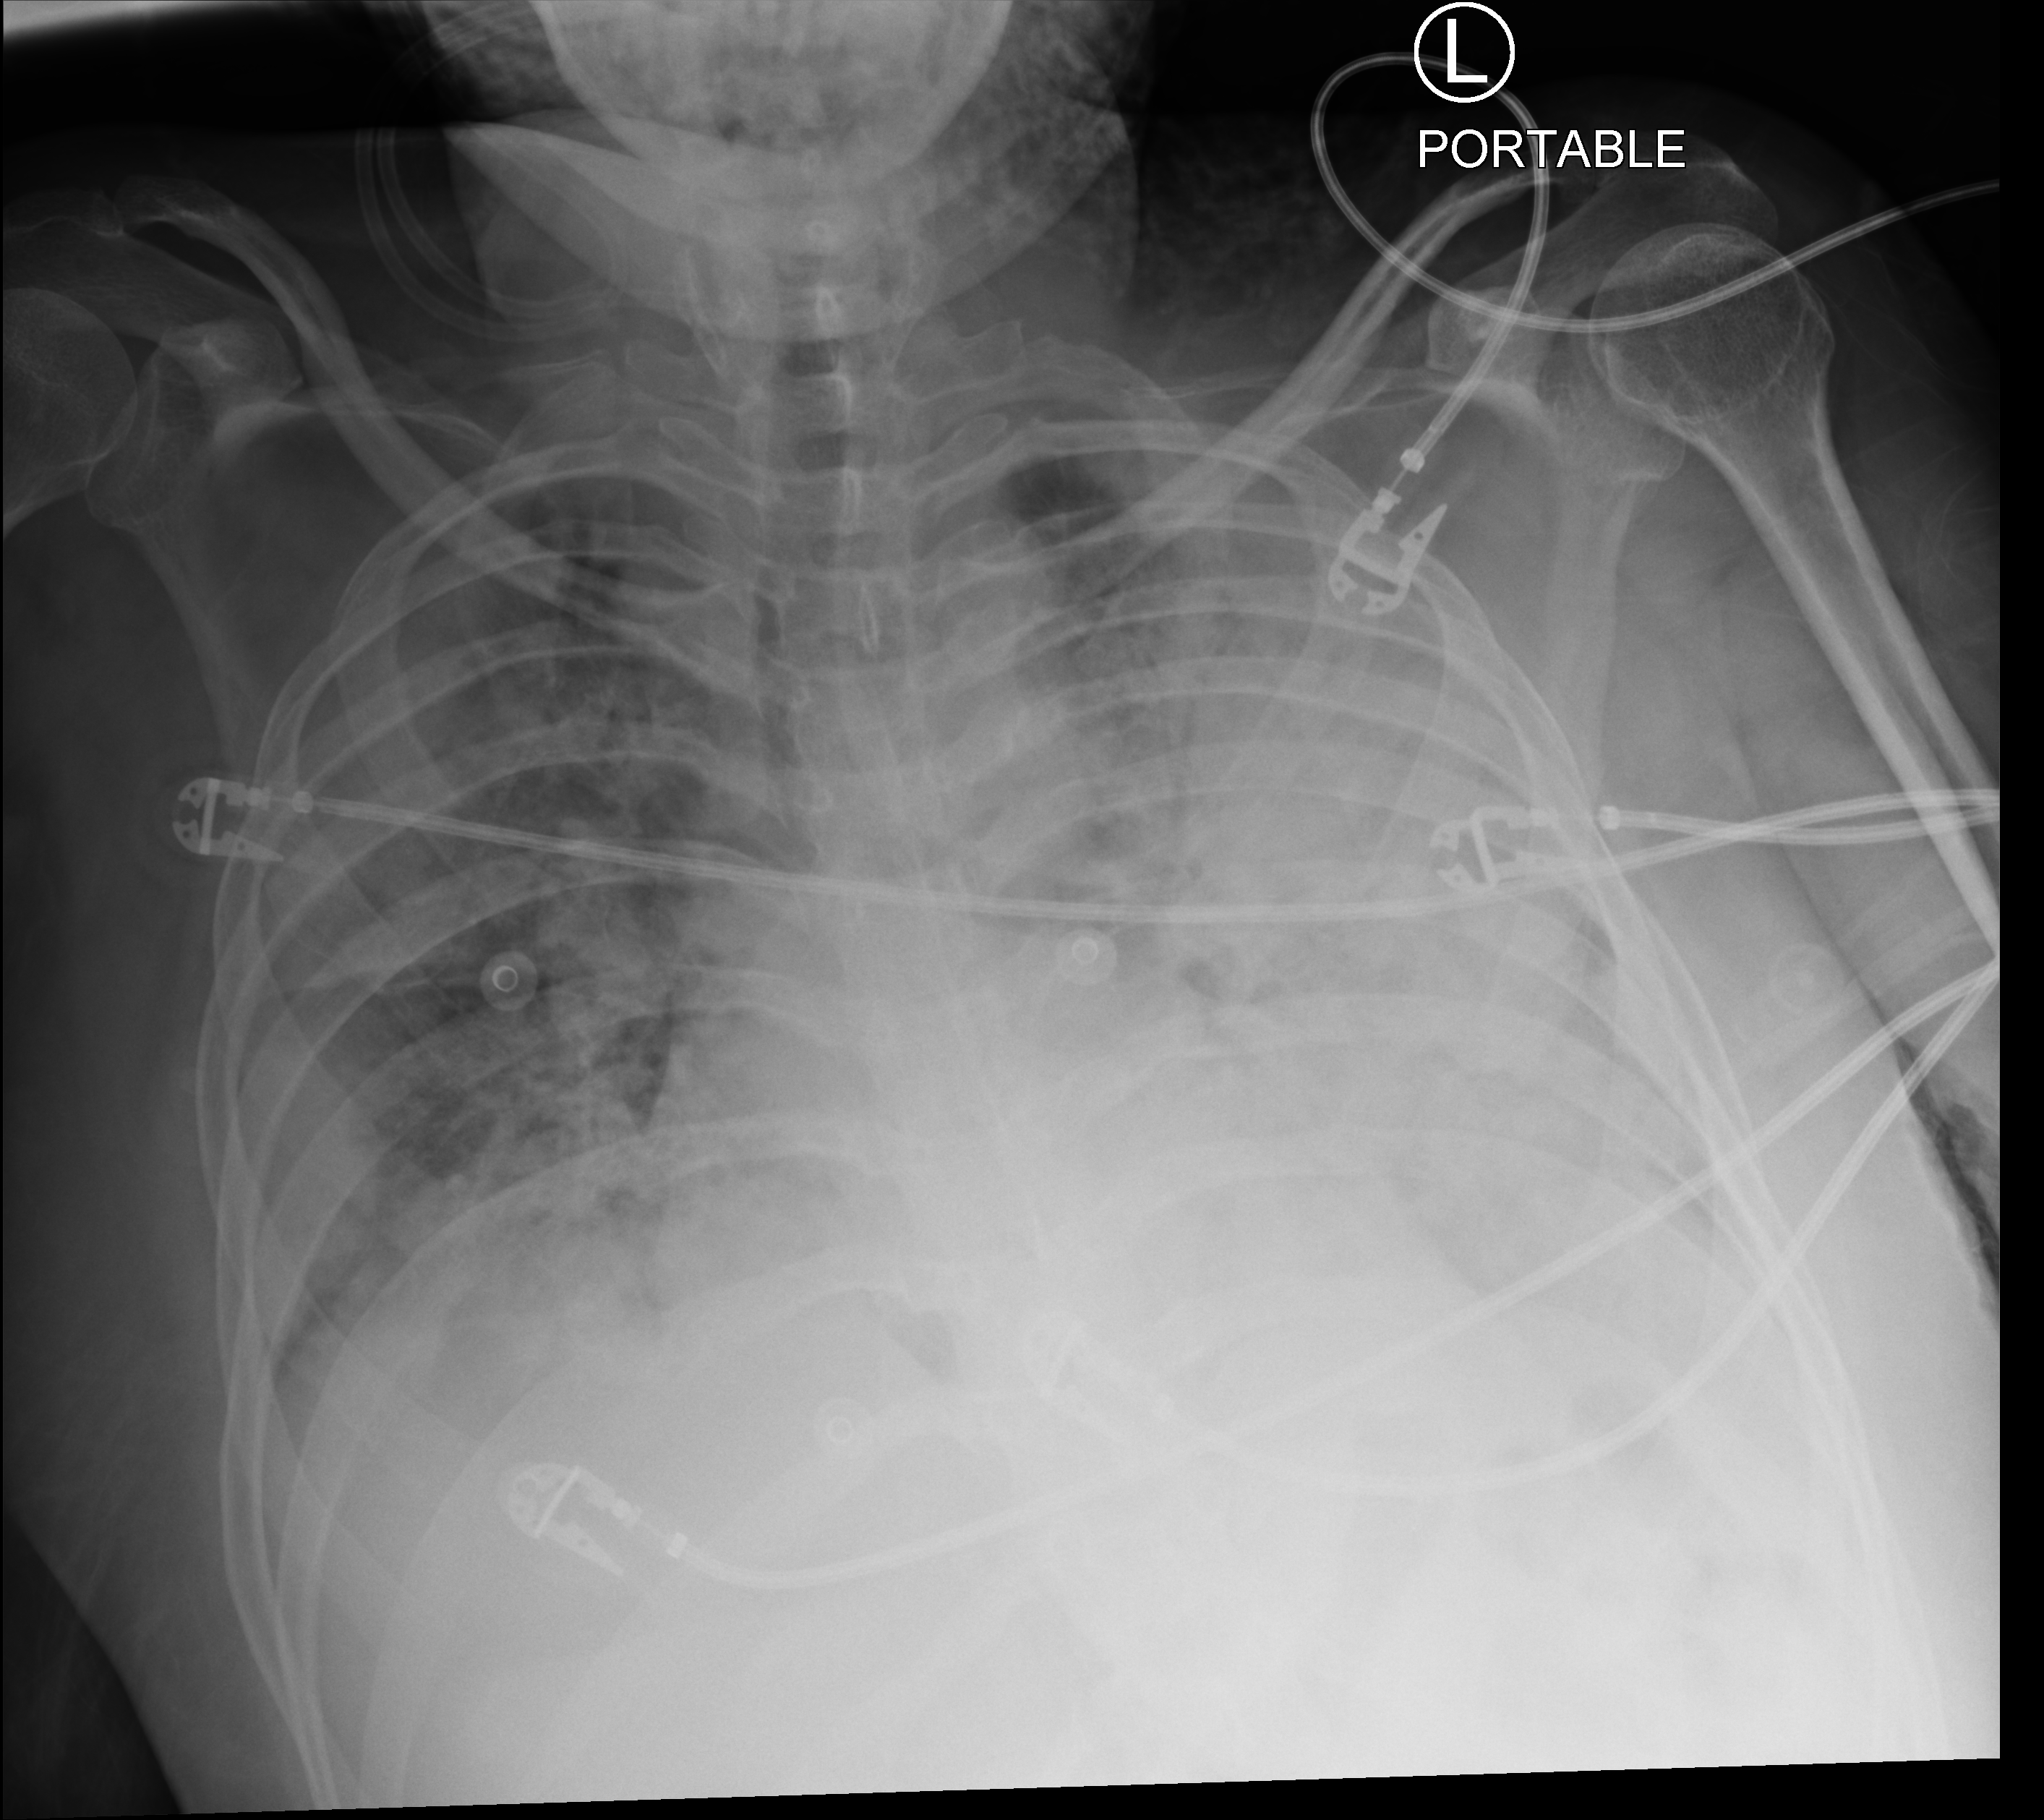
Portable chest radiograph. Adult patient hospitalised with COVID-19, age 18–59 years.
Hospital-stay facts (about this admission, not read from this image; timing relative to this image not recorded):
- mechanically ventilated during this hospital stay: yes